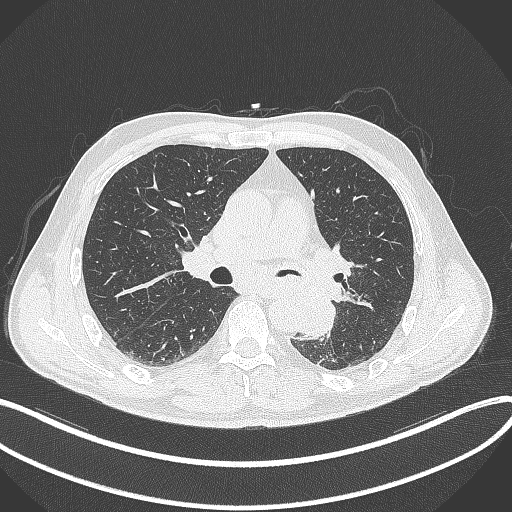
Chest CT, one axial slice. Position 199 of 329 along the scan axis. Lung window (W 1500 / L -600 HU). 1 mm slice thickness. 512 × 512 image matrix. Male patient, age 59 years. From the clinical record (not read from this slice): clinical TNM (as recorded): T2a N2 M0.
Structures marked on this image (rectangle marked by the reading radiologist):
- lung tumour (recorded histology: squamous cell carcinoma): bounding box <297,294,340,341> (left, top, right, bottom; pixels)